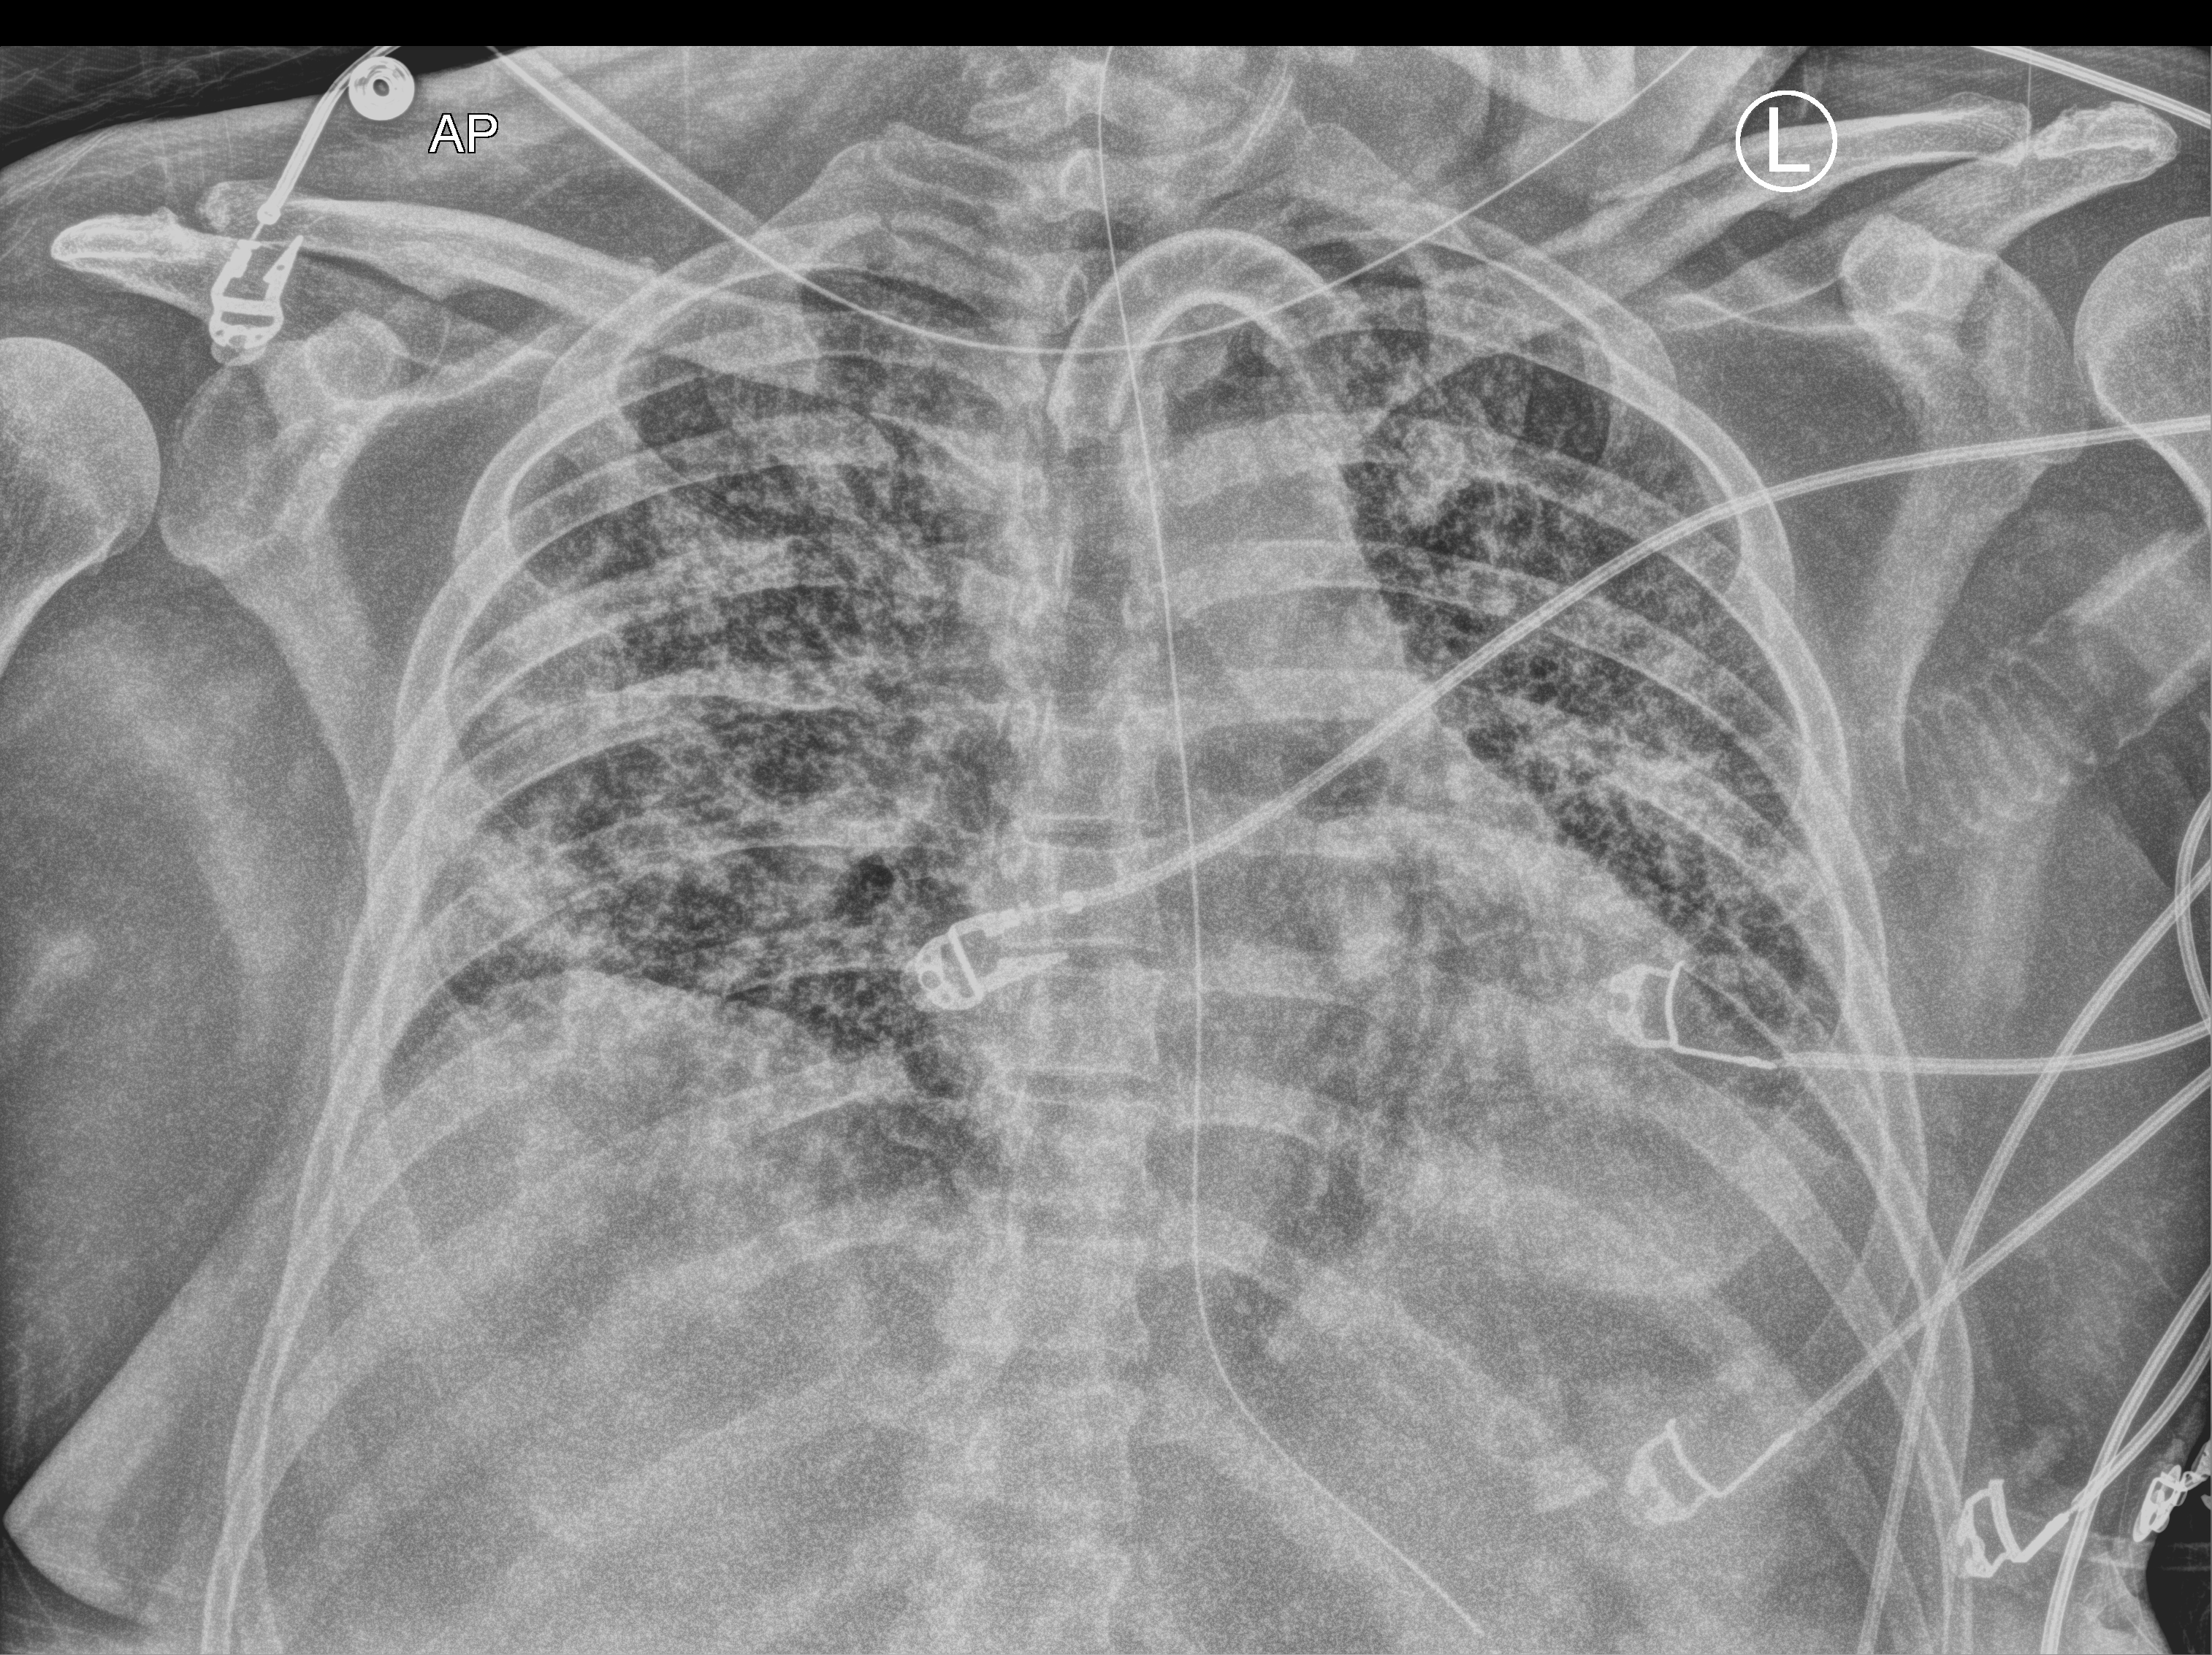
Portable chest radiograph, anteroposterior (AP) projection. Male patient hospitalised with COVID-19, age 18–59 years.
From the hospital-stay record, not from the radiograph (when in the stay this image was taken is not recorded):
- other chronic lung disease (admission record): no
- COPD (admission record): no
- mechanically ventilated during this hospital stay: yes